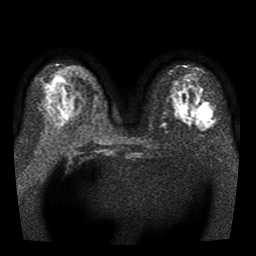
Breast MRI, one axial slice. Position 20 of 41 along the scan axis. Diffusion-weighted series; image 2 of 3 stored at this slice position (different b-values; order by instance number). 1.5 T. 5 mm slice thickness. 256 × 256 image matrix, field of view 330 × 330 mm. Female patient.
Outlined on this slice (outlined manually by an expert reader):
- tumour on diffusion-weighted imaging: bounding box (x1, y1, x2, y2) in pixels: (199, 107, 211, 120)